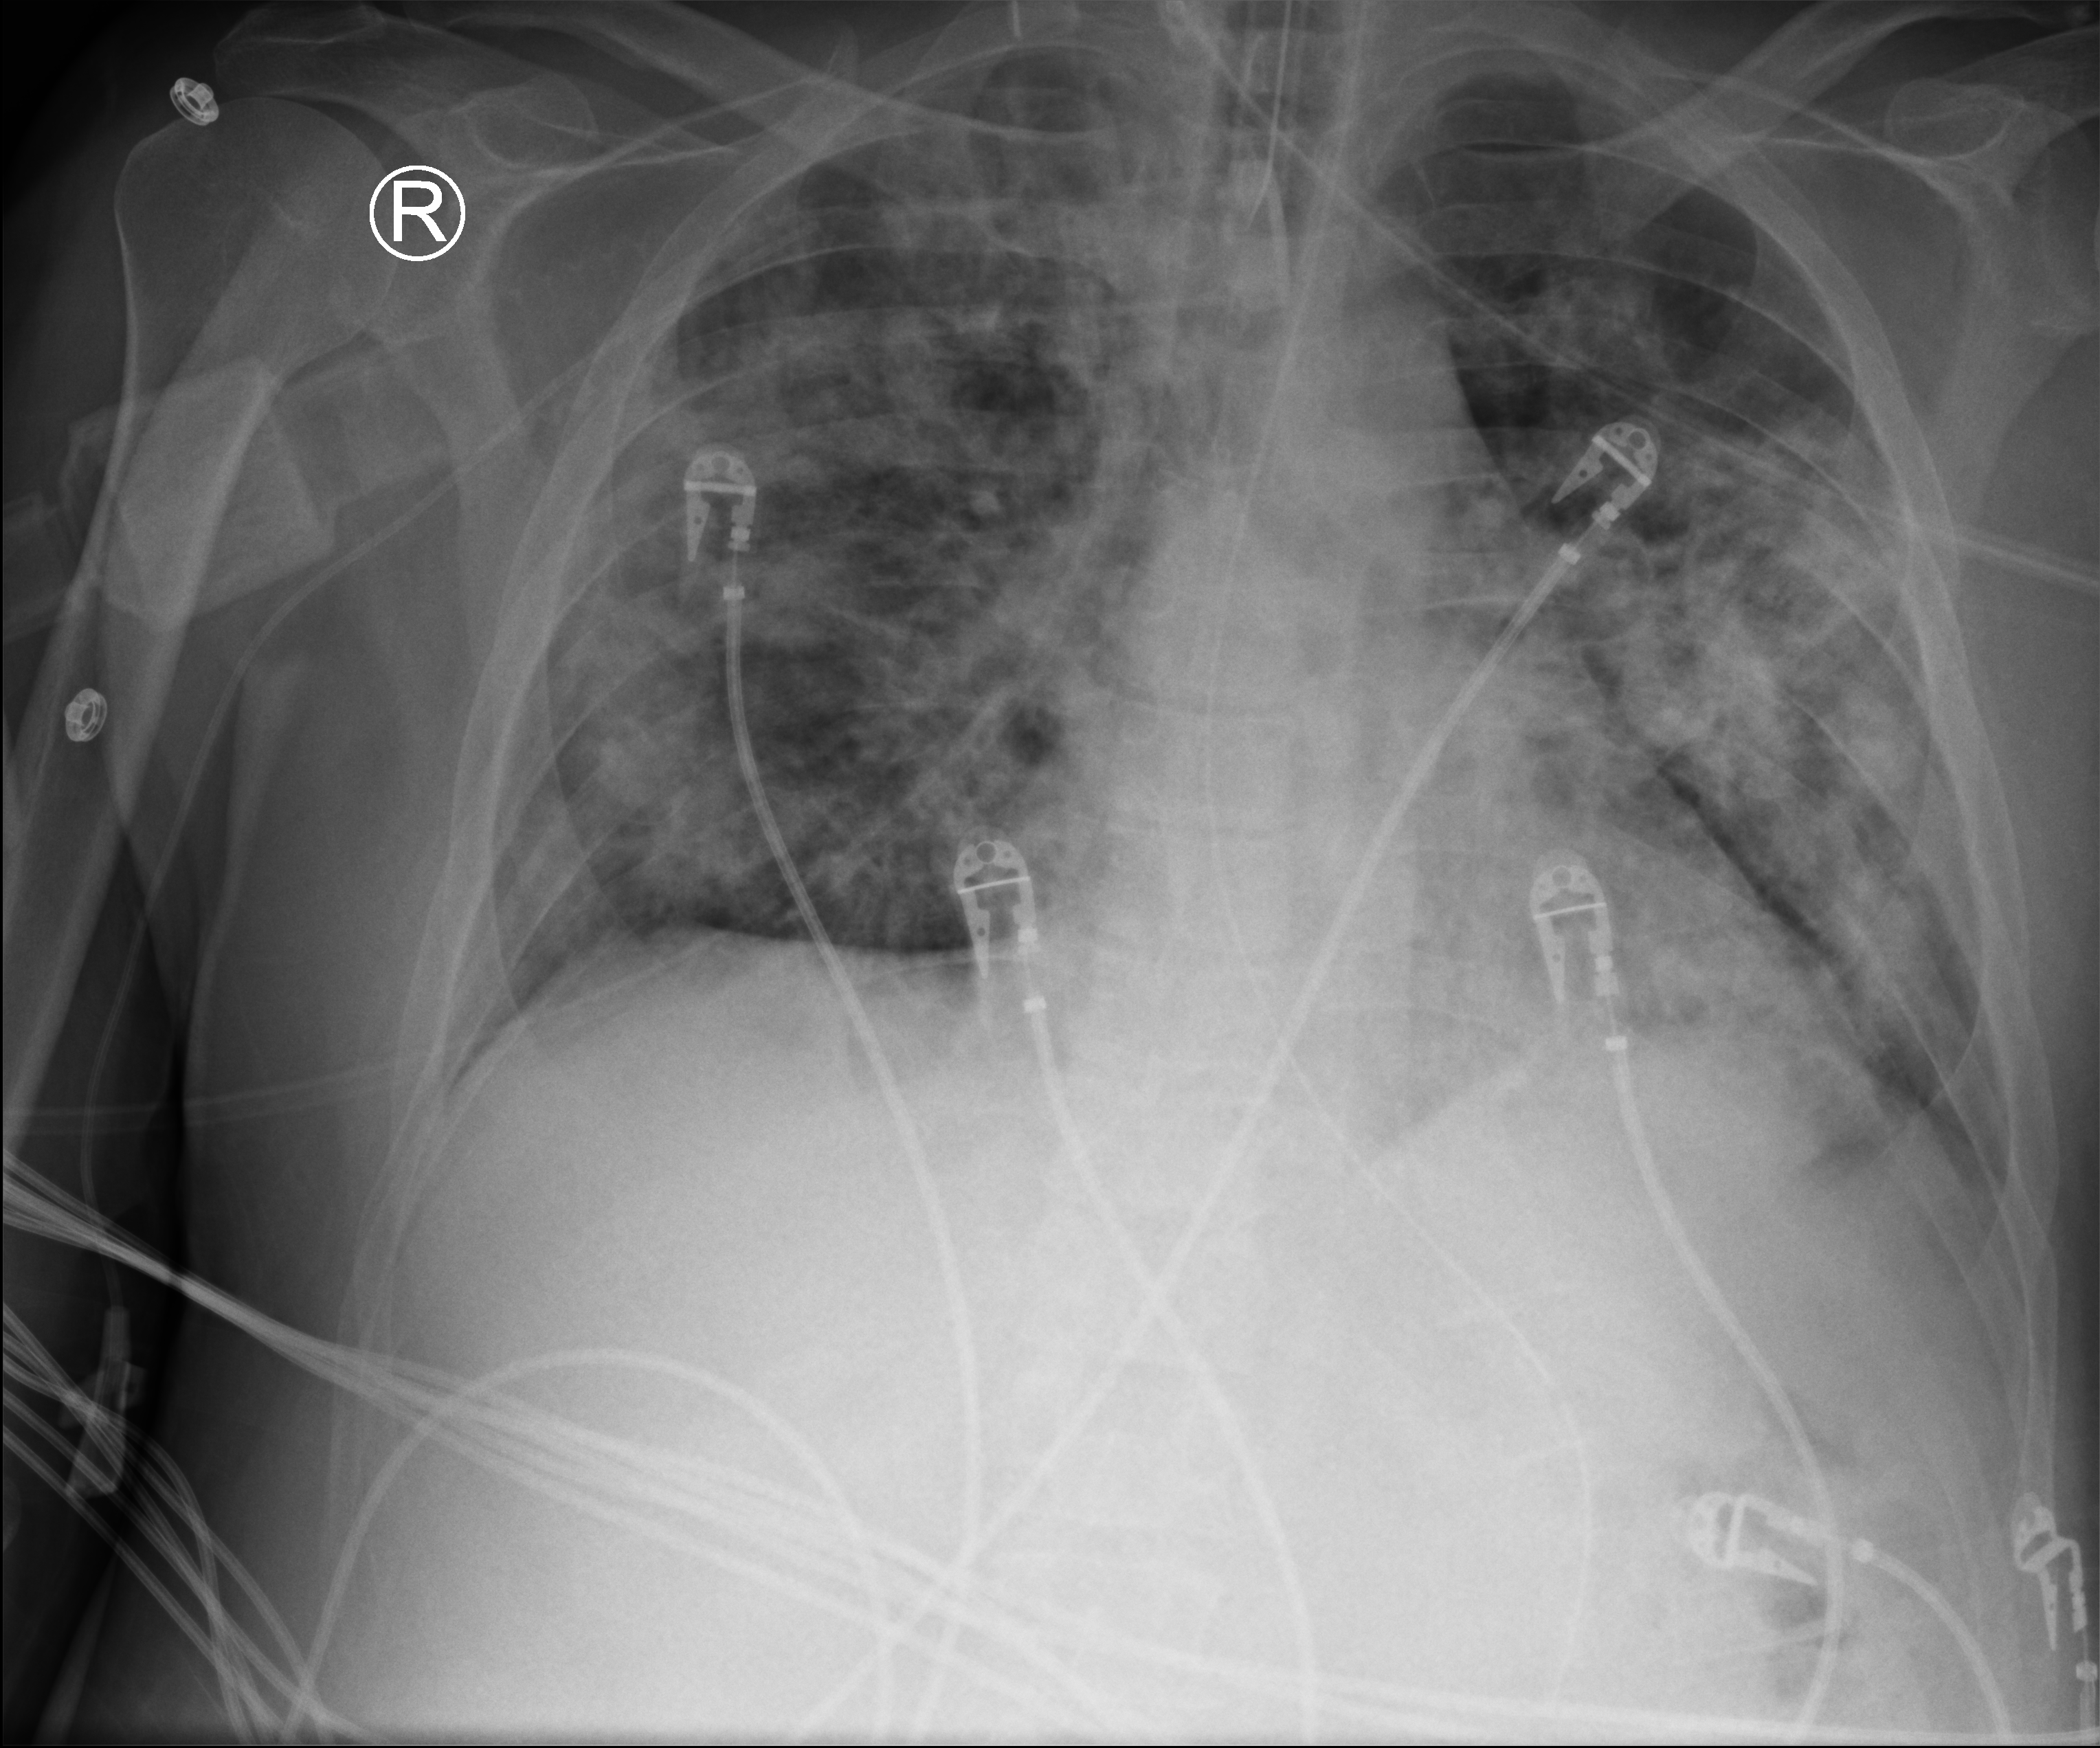
Bedside chest radiograph (computed radiography); anteroposterior (AP) projection. Male patient hospitalised with COVID-19, age 18–59 years.
Hospital-stay facts (about this admission, not read from this image; timing relative to this image not recorded):
- diabetes (admission record): yes
- other chronic lung disease (admission record): no